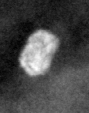
Region of interest cut from a scanned film mammogram (one marked finding); right breast; MLO view; BI-RADS breast density category 2 (scale 1–4).
Calcifications, morphology coarse / round and regular / lucent center; BI-RADS assessment category 2; subtlety rating 5 on a 1 (subtle) to 5 (obvious) scale; benign without callback (not worked up further).